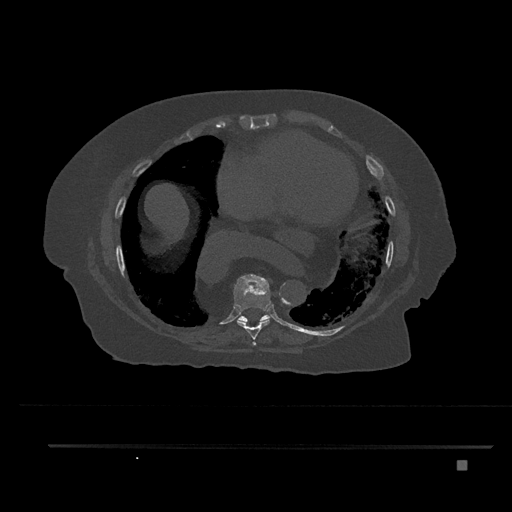
CT including the spine, one axial slice. Slice 428 of 797 in the series (ordered by position). Reconstruction kernel Br40s/3. Bone window (W 1800 / L 400 HU). 0.5 mm slice thickness. 512 × 512 image matrix. Female patient, age 76 years. From the clinical record (not read from this slice): primary cancer: lung; vertebrae with lytic lesions (as recorded): T11, L3.
Annotated regions visible in this slice (semi-automatically segmented with operator editing):
- T7 vertebra: bounding box <253,342,256,345> (left, top, right, bottom; pixels)
- T8 vertebra: <234,274,271,346>
- T9 vertebra: <237,311,271,322>